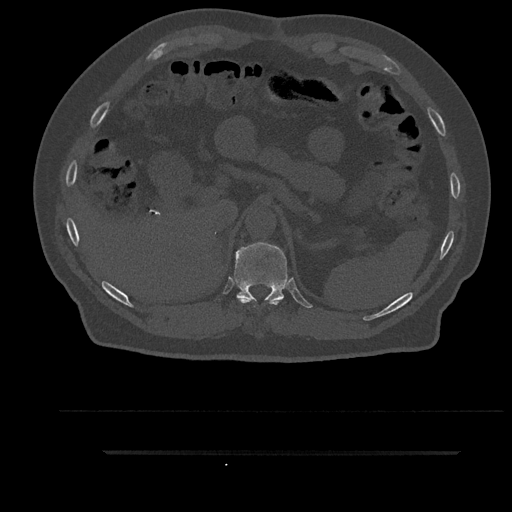
CT including the spine, one axial slice. Slice 328 of 797 in the series (ordered by position). Reconstruction kernel Br40s/3. 120 kVp. Bone window (W 1800 / L 400 HU). 0.5 mm slice thickness. 512 × 512 image matrix, field of view 432 × 432 mm. Patient: male, 63 years. Case-level facts recorded for this patient, not image findings: primary cancer: renal.
Structures marked on this image (semi-automatic segmentation, software-assisted and operator-edited):
- T10 vertebra: bounding box (x1, y1, x2, y2) in pixels: (238, 298, 279, 307)
- T11 vertebra: (234, 241, 288, 302)